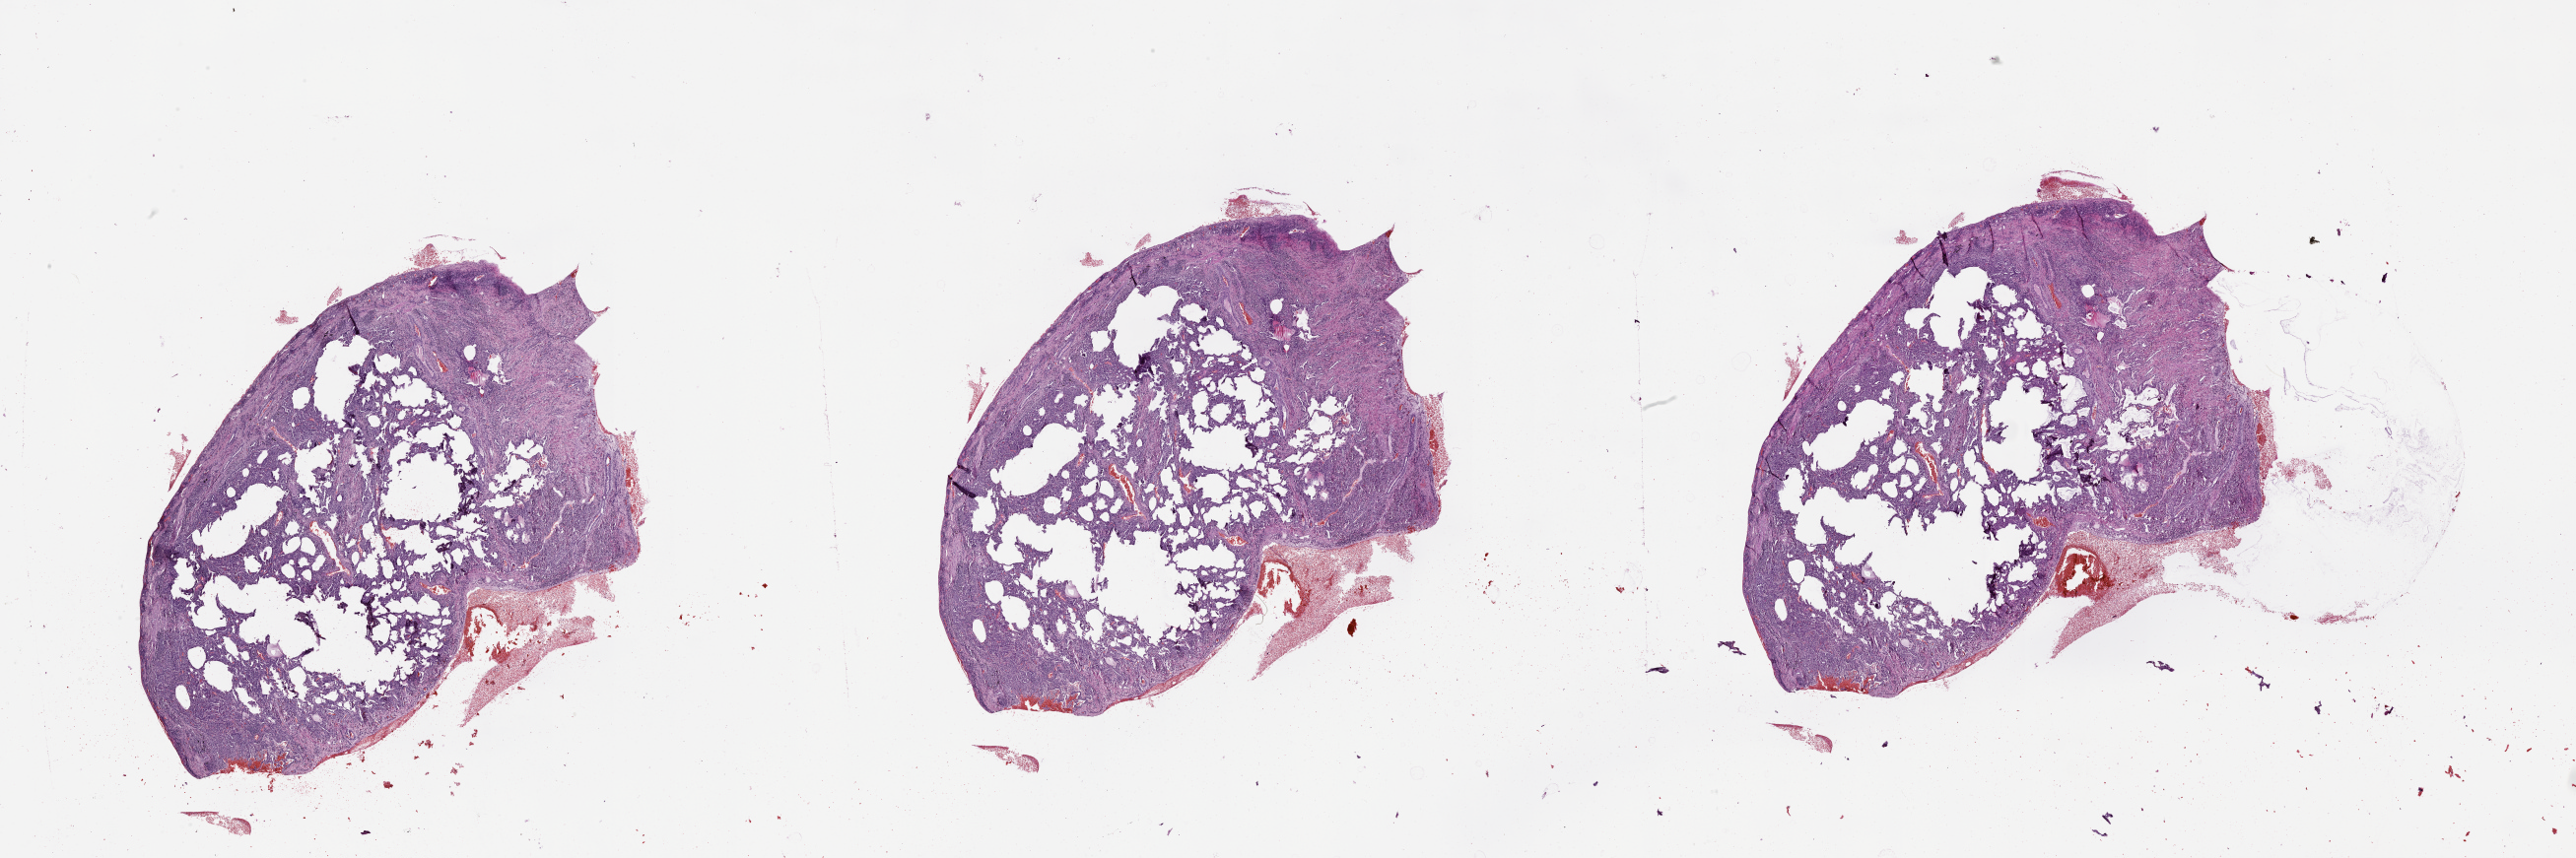
H&E-stained whole-slide image, shown as a low-resolution overview of the whole scanned area (about 42.1 x 14.0 mm, acquisition: 20x scan), lung, normal (non-tumour) tissue. Patient: male, age 49 years.
* this section: normal (non-tumour) tissue from the same patient
* patient diagnosis (cohort enrolment): squamous cell carcinoma (lung)